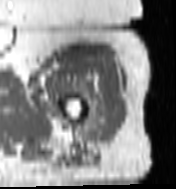
MRI of an extremity soft-tissue mass, one axial slice; position 90 of 100 along the scan axis; MR volume resampled by the dataset authors to the PET/CT grid (not the native acquisition matrix); 3.27 mm slice thickness; 176 × 189 image matrix, field of view 172 × 185 mm. Female patient. From the clinical record (not read from this slice): histological type: undifferentiated – high grade; grade: high; site of the primary tumour: left thigh.
Outlined on this slice (expert contour drawn on MRI and transferred to this co-registered scan by the dataset authors):
- gross tumour volume including surrounding oedema: box from (x=78, y=89) to (x=111, y=142) px
- gross tumour volume (mass): (x=89, y=119)–(x=102, y=124)